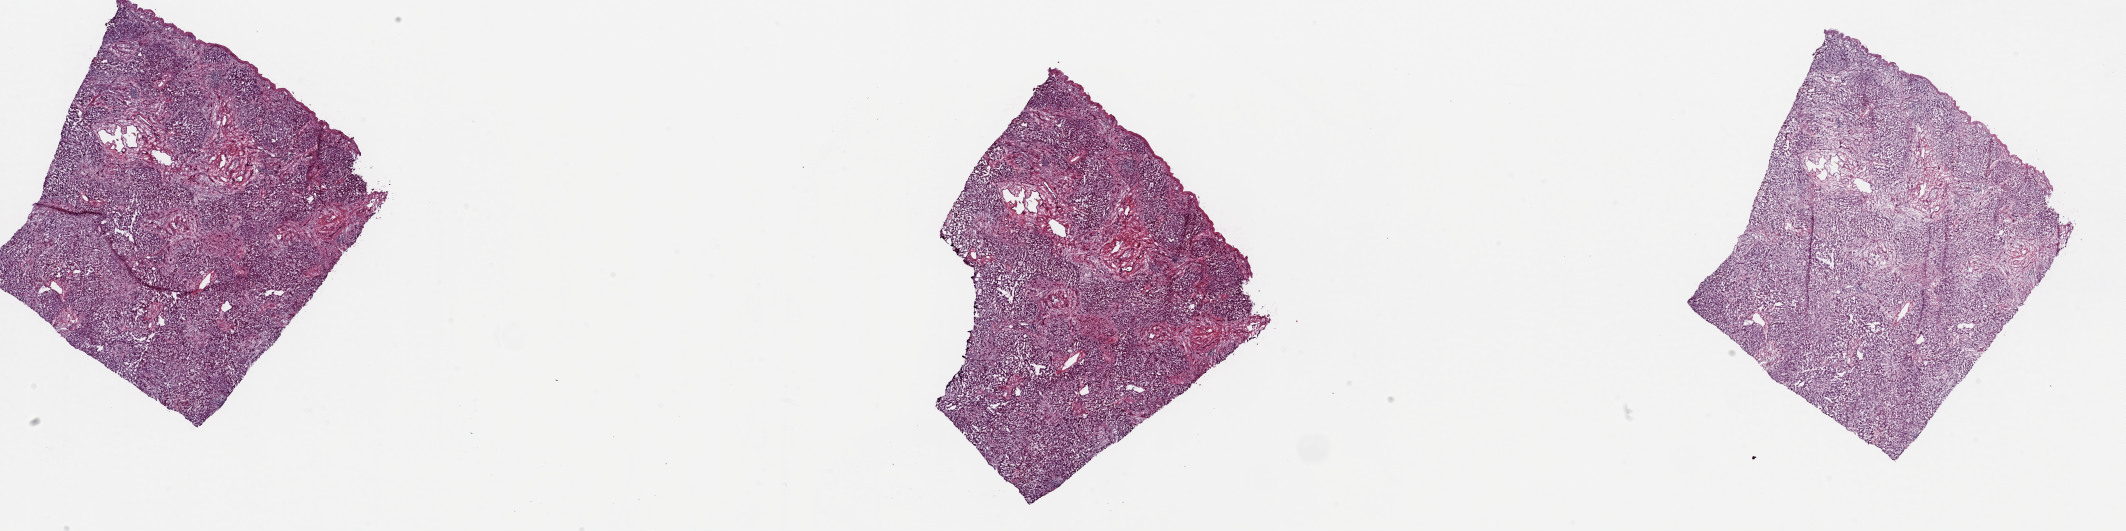
H&E whole-slide image, whole scanned area (about 33.7 x 8.4 mm, from a 20x scan) shown as a low-resolution overview; frozen section; sample: solid tissue normal (non-tumour tissue), liver. Male, age 78 years at initial diagnosis. Composition of this section per pathologist review: tumour cells 0%, tumour nuclei 0%, normal cells 75%, stromal cells 25%, necrosis 0%. Inflammatory infiltration, as recorded: lymphocyte infiltration 5%, monocyte infiltration 1%, neutrophil infiltration 1%.
This section: solid tissue normal sample (biorepository sample class). Patient diagnosis: Hepatocellular carcinoma, NOS.